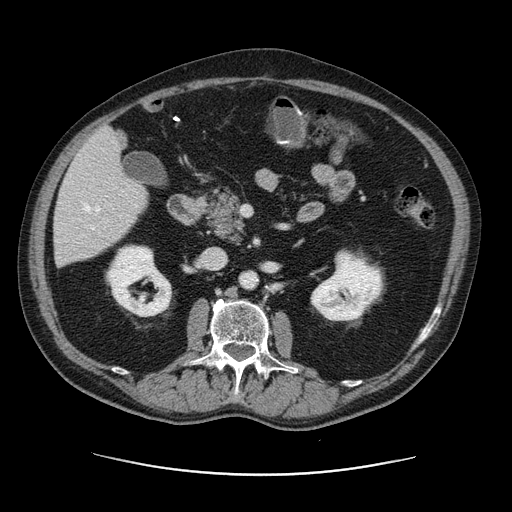
Contrast-enhanced abdominal CT, one axial slice; position 52 of 141 along the scan axis; 120 kVp; soft-tissue window (W 400 / L 40 HU); 512 × 512 image matrix. Male patient, age 72 years. Case-level facts recorded for this patient, not image findings: diagnosis: colorectal cancer liver metastases, imaged before liver resection.
Outlined on this slice (outlined manually by an expert reader):
- hepatic veins: bounding box <84,204,100,229> (left, top, right, bottom; pixels)
- liver: <54,129,147,265>
- planned liver remnant (the part of the liver to remain after resection): <54,173,147,265>